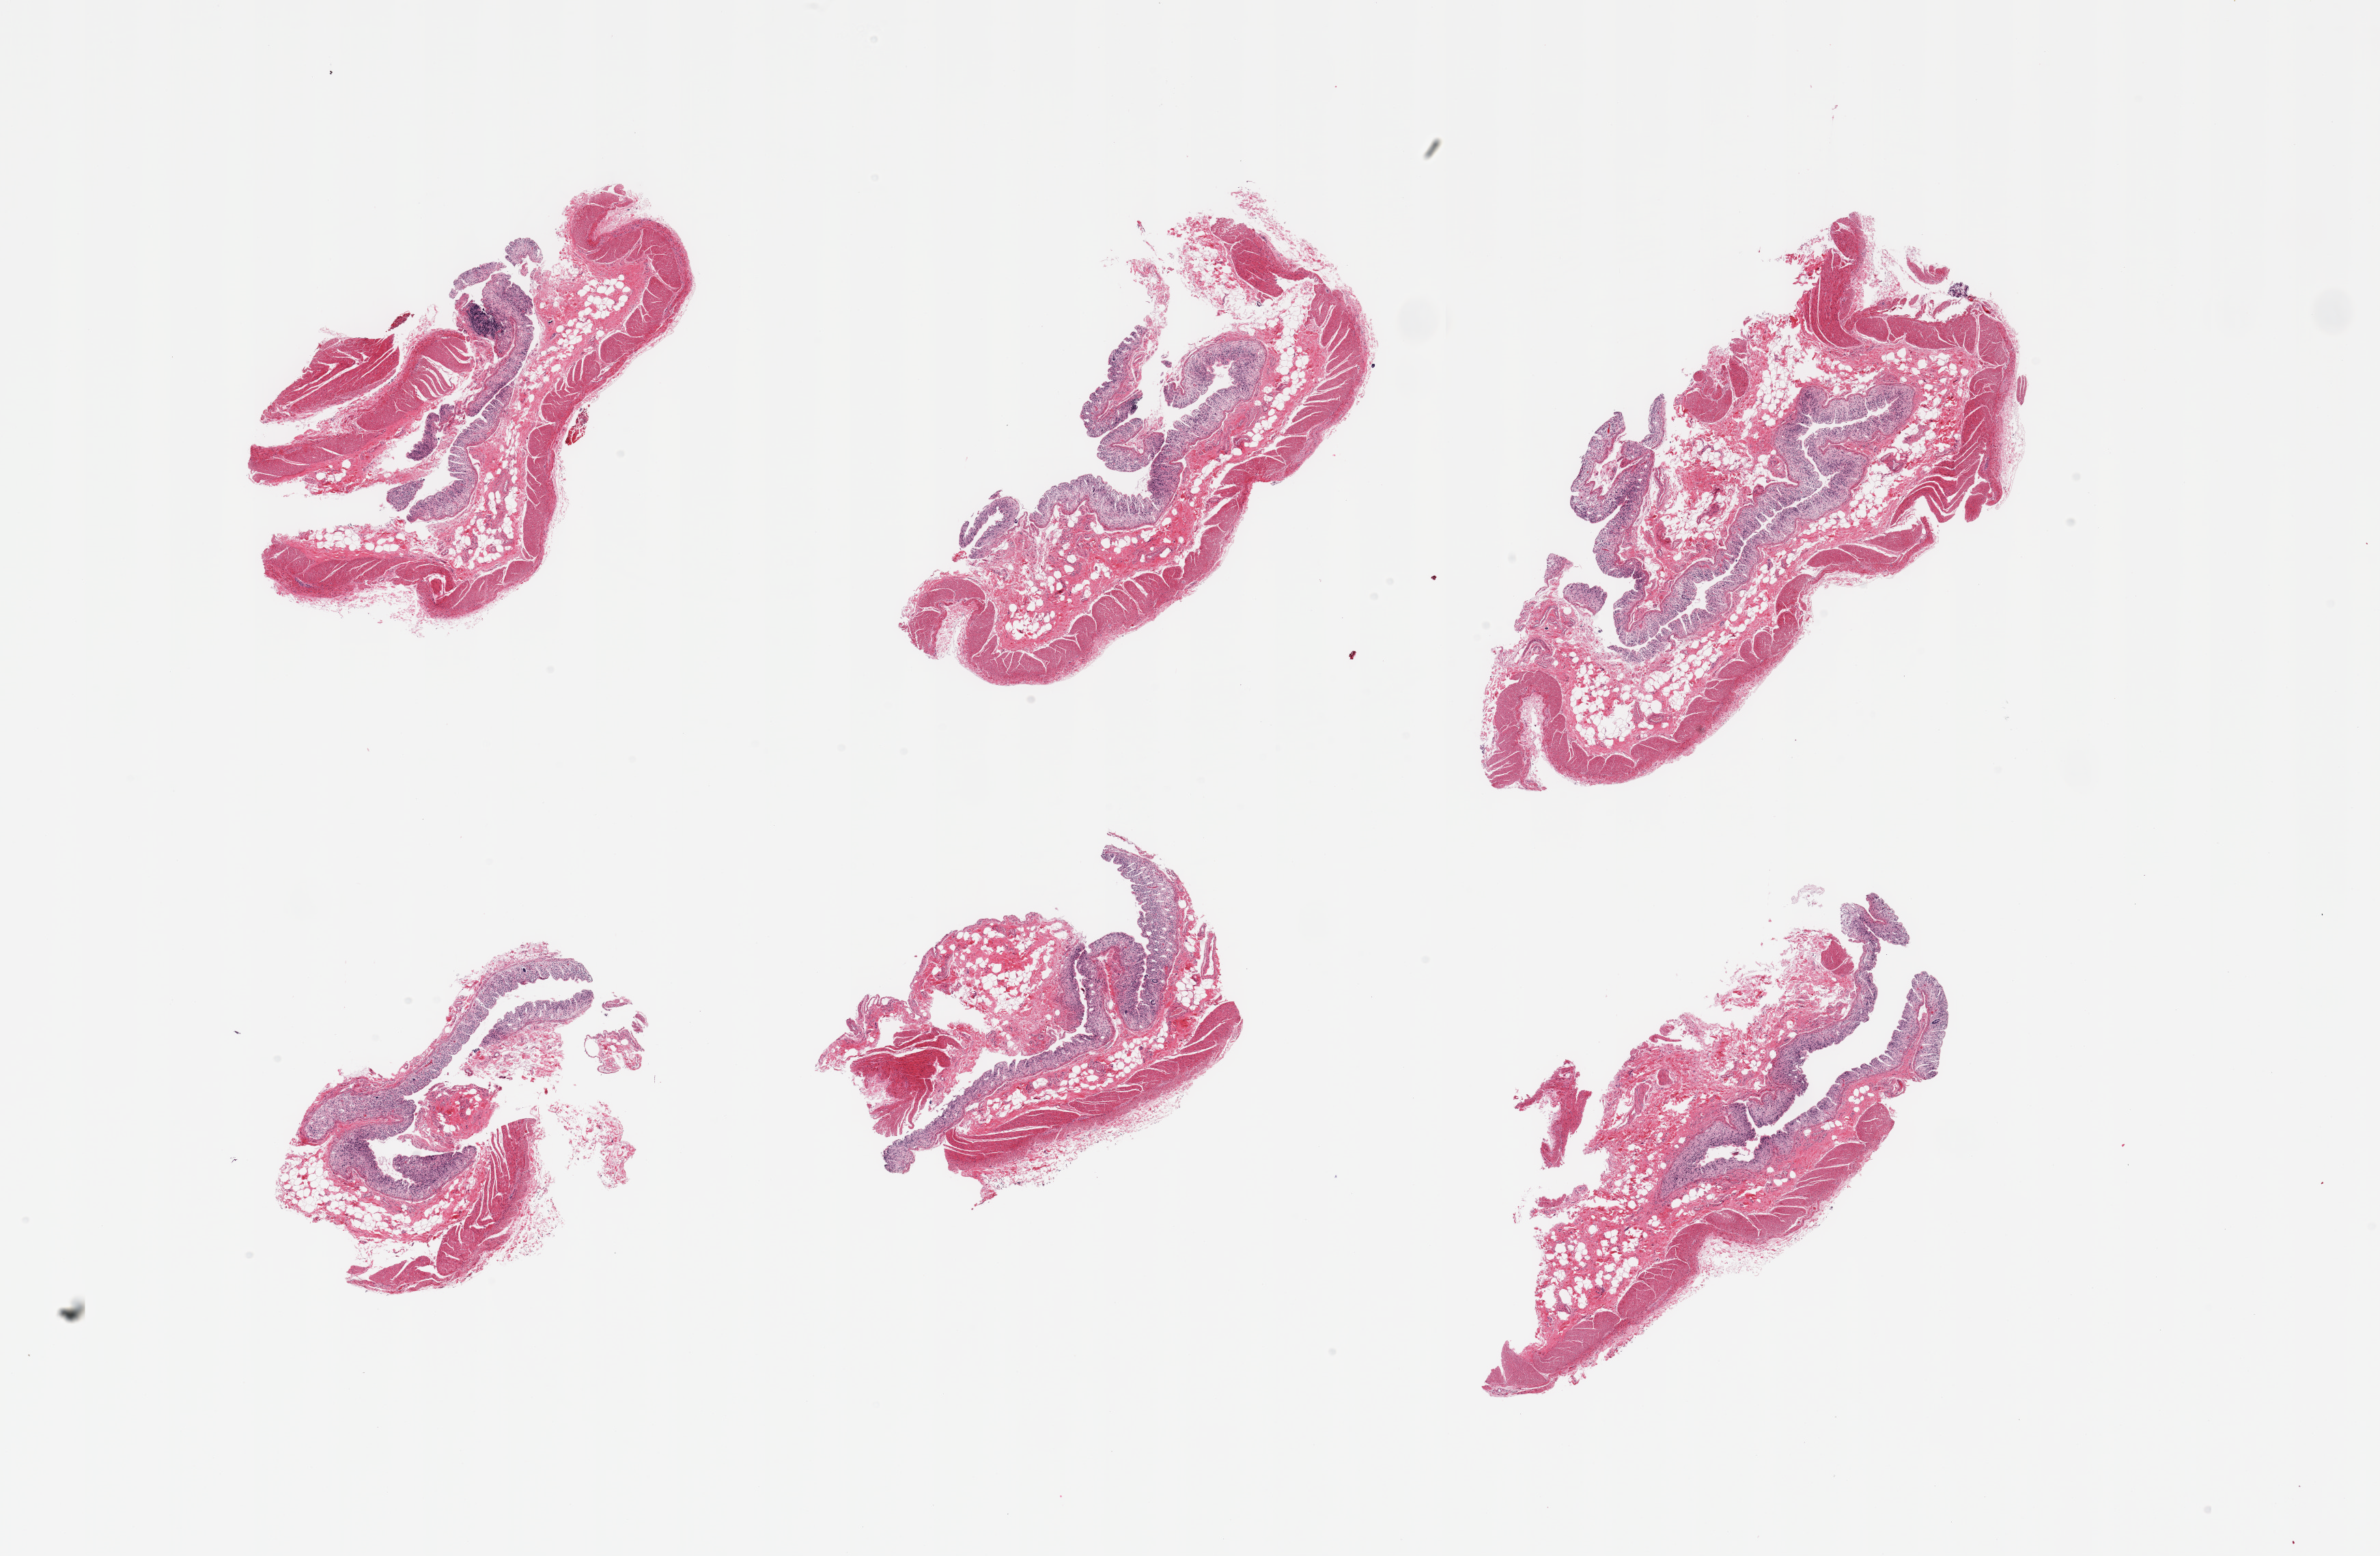
Hematoxylin and eosin (H&E) whole-slide image, brightfield, a low-resolution overview of the entire scanned area, about 27.6 x 18.0 mm (acquisition: 20x scan), PAXgene-fixed, paraffin-embedded tissue, section of transverse colon (target tissue), tissue donor sample. Donor sex: male.
Reviewer comment on this tissue sample: 6 pieces, mucosa completely autolyzed.